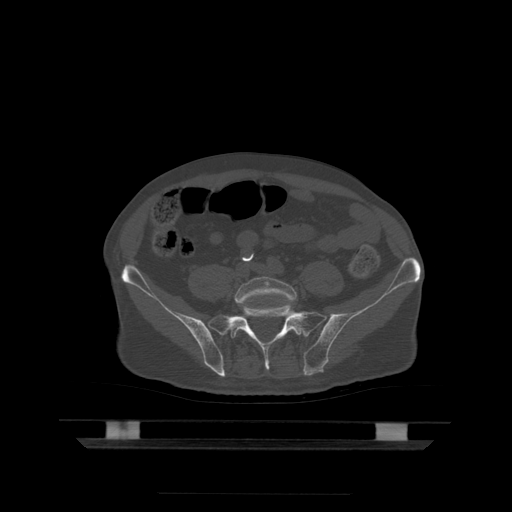
CT including the spine, one axial slice. Position 61 of 522 along the scan axis. Bone window (W 1800 / L 400 HU). 512 × 512 image matrix, field of view 436 × 436 mm. Patient age 68 years. From the clinical record (not read from this slice): primary cancer: urothelial.
Structures marked on this image (semi-automatic segmentation, software-assisted and operator-edited):
- L5 vertebra: bounding box <235,277,297,307> (left, top, right, bottom; pixels)